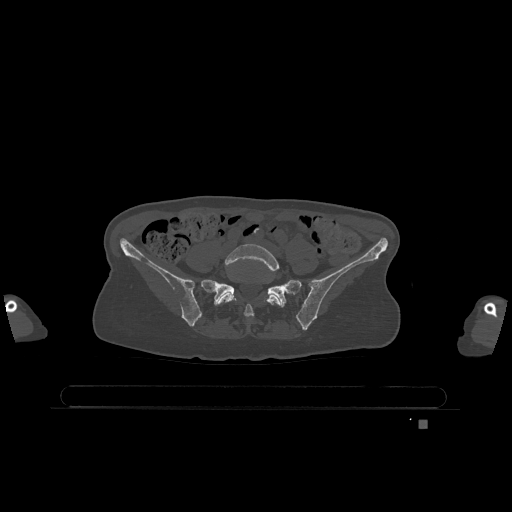
CT including the spine, one axial slice. Position 216 of 1317 along the scan axis. Bone window (W 1800 / L 400 HU). 0.5 mm slice thickness. 512 × 512 image matrix, field of view 500 × 500 mm. Patient: female, 74 years. Case-level facts recorded for this patient, not image findings: primary cancer: lung.
Structures marked on this image (semi-automatically segmented with operator editing):
- L5 vertebra: bounding box <217,244,281,317> (left, top, right, bottom; pixels)